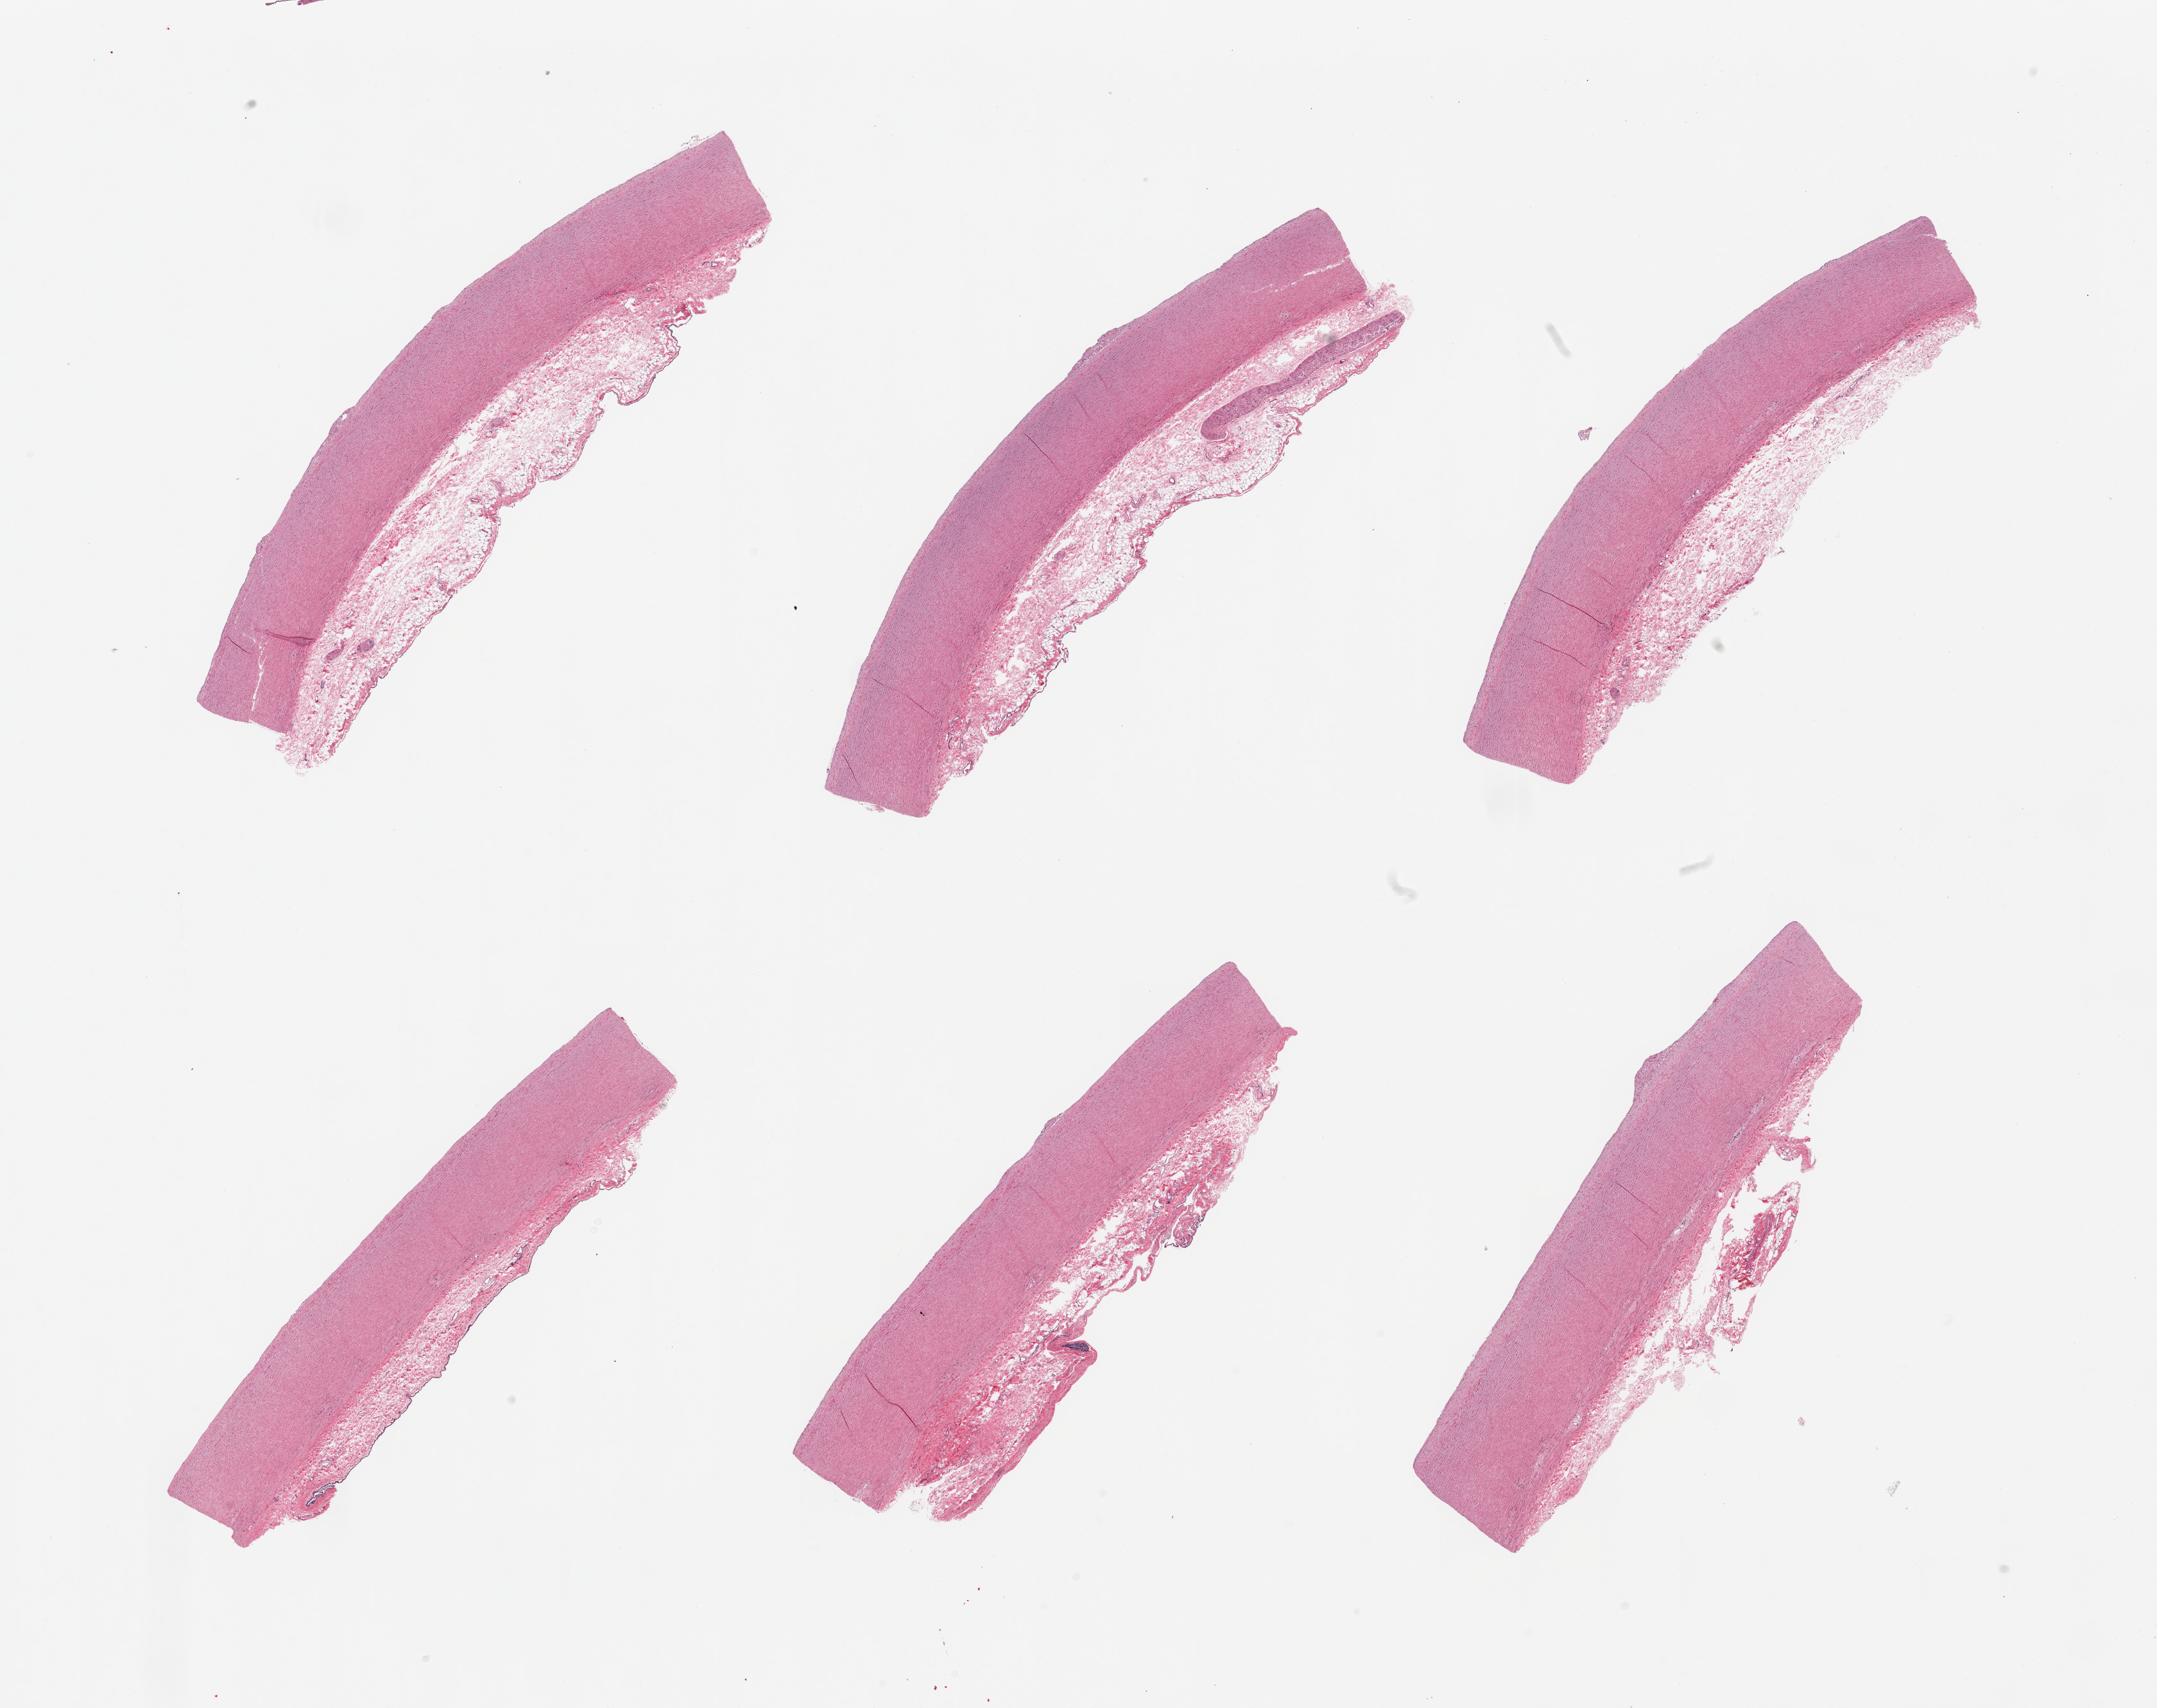
Whole-slide image, haematoxylin and eosin stain, brightfield — low-resolution overview of the scanned area, about 26.6 x 21.0 mm (acquisition: 20x scan). PAXgene-fixed paraffin-embedded (PFPE) section. Target tissue: aorta. Tissue donor sample.
Pathologist's review note for this sample: 6 pieces; includes significant residual/untrimmed adventitia.